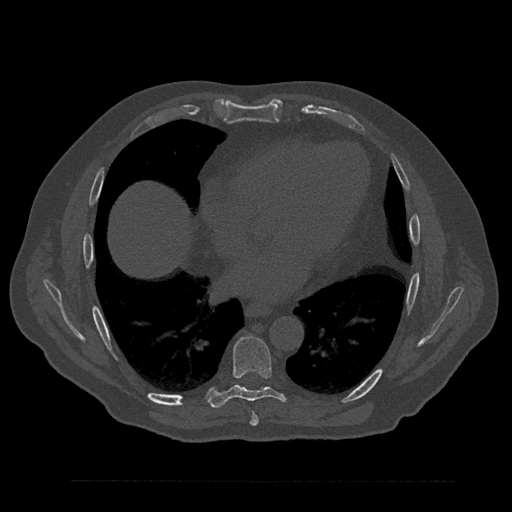
CT including the spine, one axial slice. Slice 456 of 797 in the series (ordered by position). Reconstruction kernel Br40s/3. Bone window (W 1800 / L 400 HU). 512 × 512 image matrix, field of view 430 × 430 mm. Male patient, age 61 years. From the clinical record (not read from this slice): primary cancer: prostate.
Annotated regions visible in this slice (semi-automatically segmented with operator editing):
- T7 vertebra: box from (x=250, y=413) to (x=259, y=426) px
- T8 vertebra: (x=209, y=336)–(x=287, y=408)